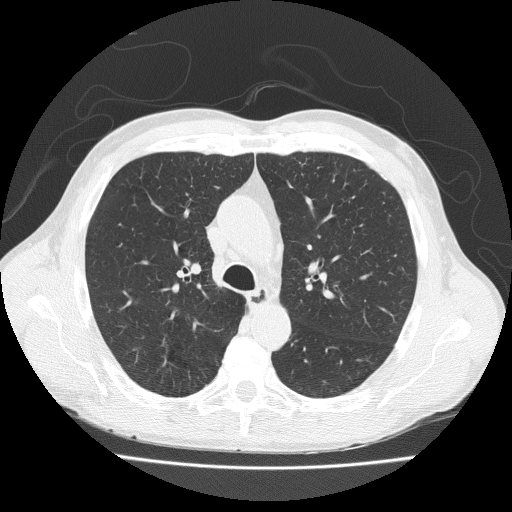
Low-dose screening chest CT, axial slice; first (baseline) screen; lung window (W 1500 / L -600 HU); lung (sharp) reconstruction kernel (FC51); slice 66 of 203 in the series; 512 × 512 image matrix, field of view 370 × 370 mm. Male, age 73 years at enrolment. Current smoker at enrolment.
• Lesion marked by an expert reader, bounding box [x1, y1, x2, y2] px = [145, 341, 200, 390].
• Screening reader's record for this exam: no non-calcified nodule ≥4 mm recorded.
• Later outcome: lung cancer diagnosed 777 days after this screen (after the third annual screen) — adenosquamous carcinoma, right upper lobe, well differentiated (G1), stage IA (AJCC 6th edition), 20 mm at pathology.